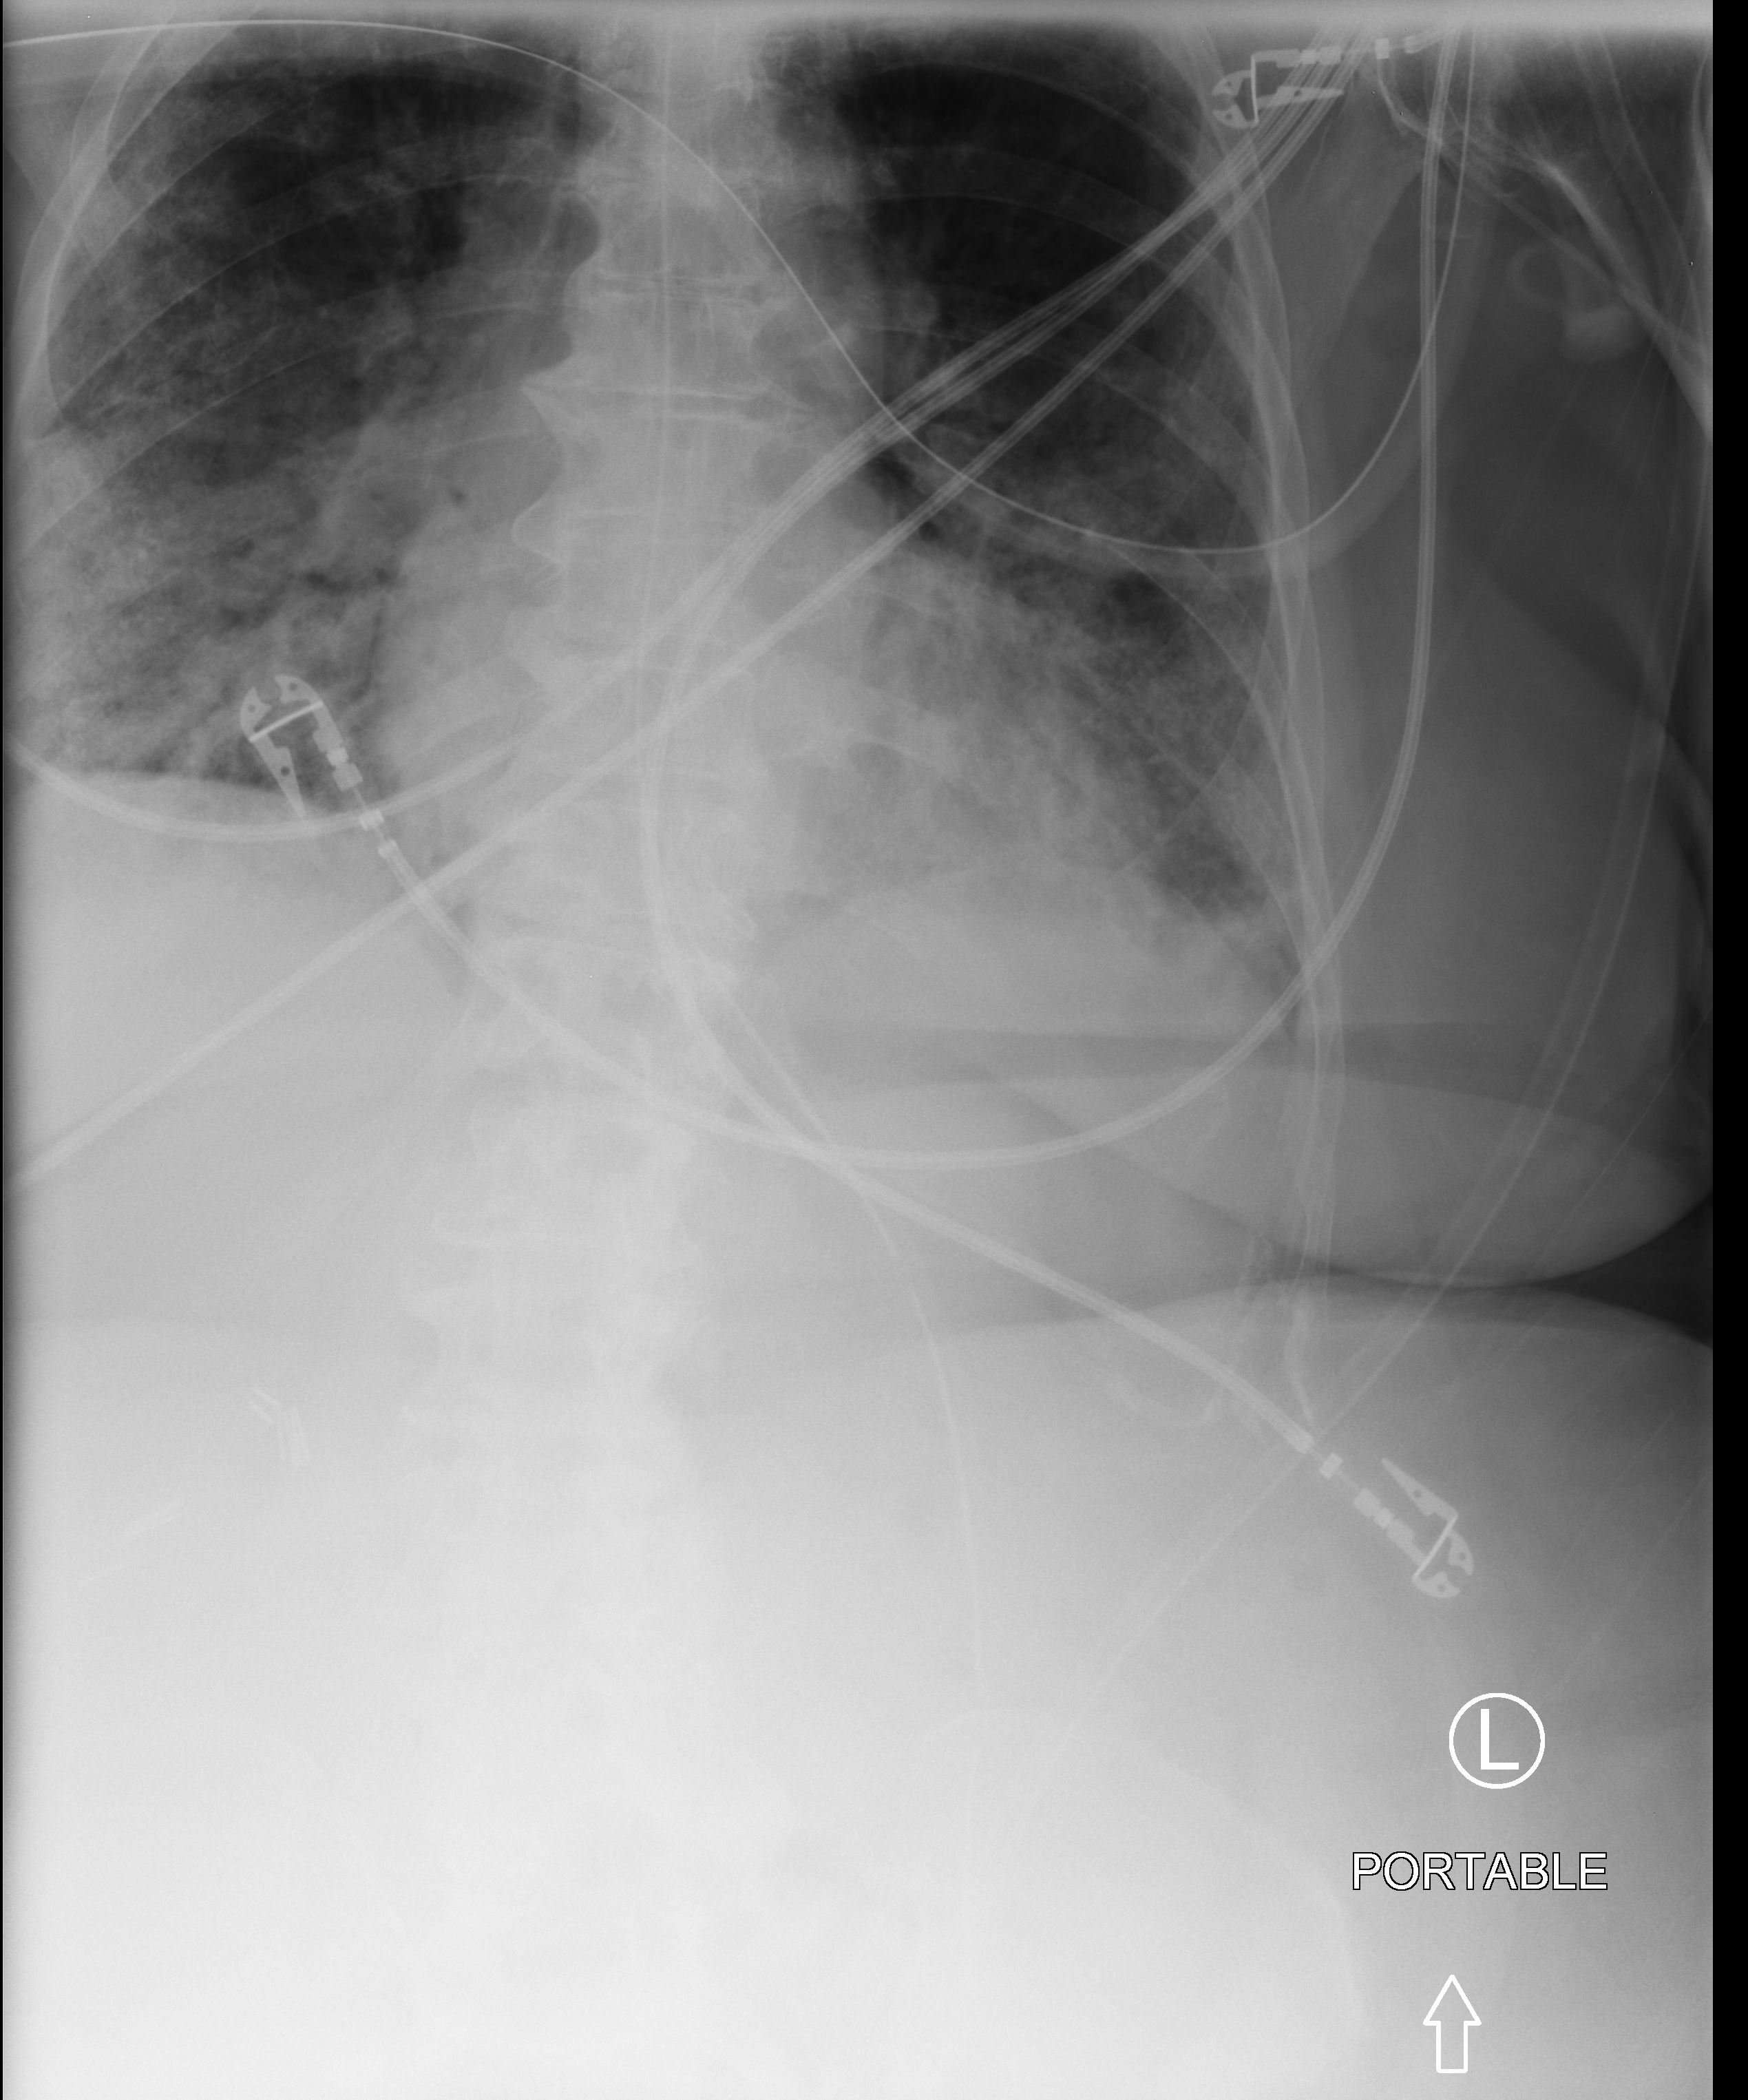
Portable abdomen radiograph. Female patient hospitalised with COVID-19, age 75–90 years.
Hospital-stay facts (about this admission, not read from this image; timing relative to this image not recorded):
- mechanically ventilated during this hospital stay: yes
- chronic kidney disease (admission record): no